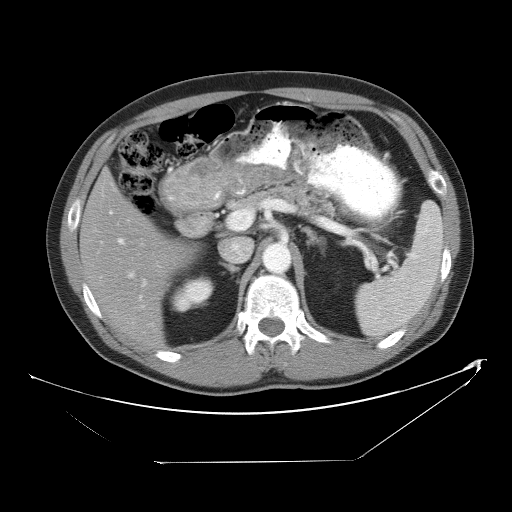
Contrast-enhanced abdominal CT, one axial slice. Position 30 of 53 along the scan axis. 120 kVp. Soft-tissue window (W 400 / L 40 HU). 5 mm slice thickness. 512 × 512 image matrix, field of view 438 × 438 mm. Male patient, age 59 years. Case-level facts recorded for this patient, not image findings: diagnosis: colorectal cancer liver metastases, imaged before liver resection; multiple liver metastases: yes; largest metastasis: 8.5 cm.
Outlined on this slice (expert manual segmentation):
- hepatic veins: bounding box (x1, y1, x2, y2) in pixels: (109, 210, 135, 278)
- liver: (81, 174, 193, 348)
- planned liver remnant (the part of the liver to remain after resection): (81, 174, 193, 349)
- portal vein (with intrahepatic branches): (118, 211, 253, 299)